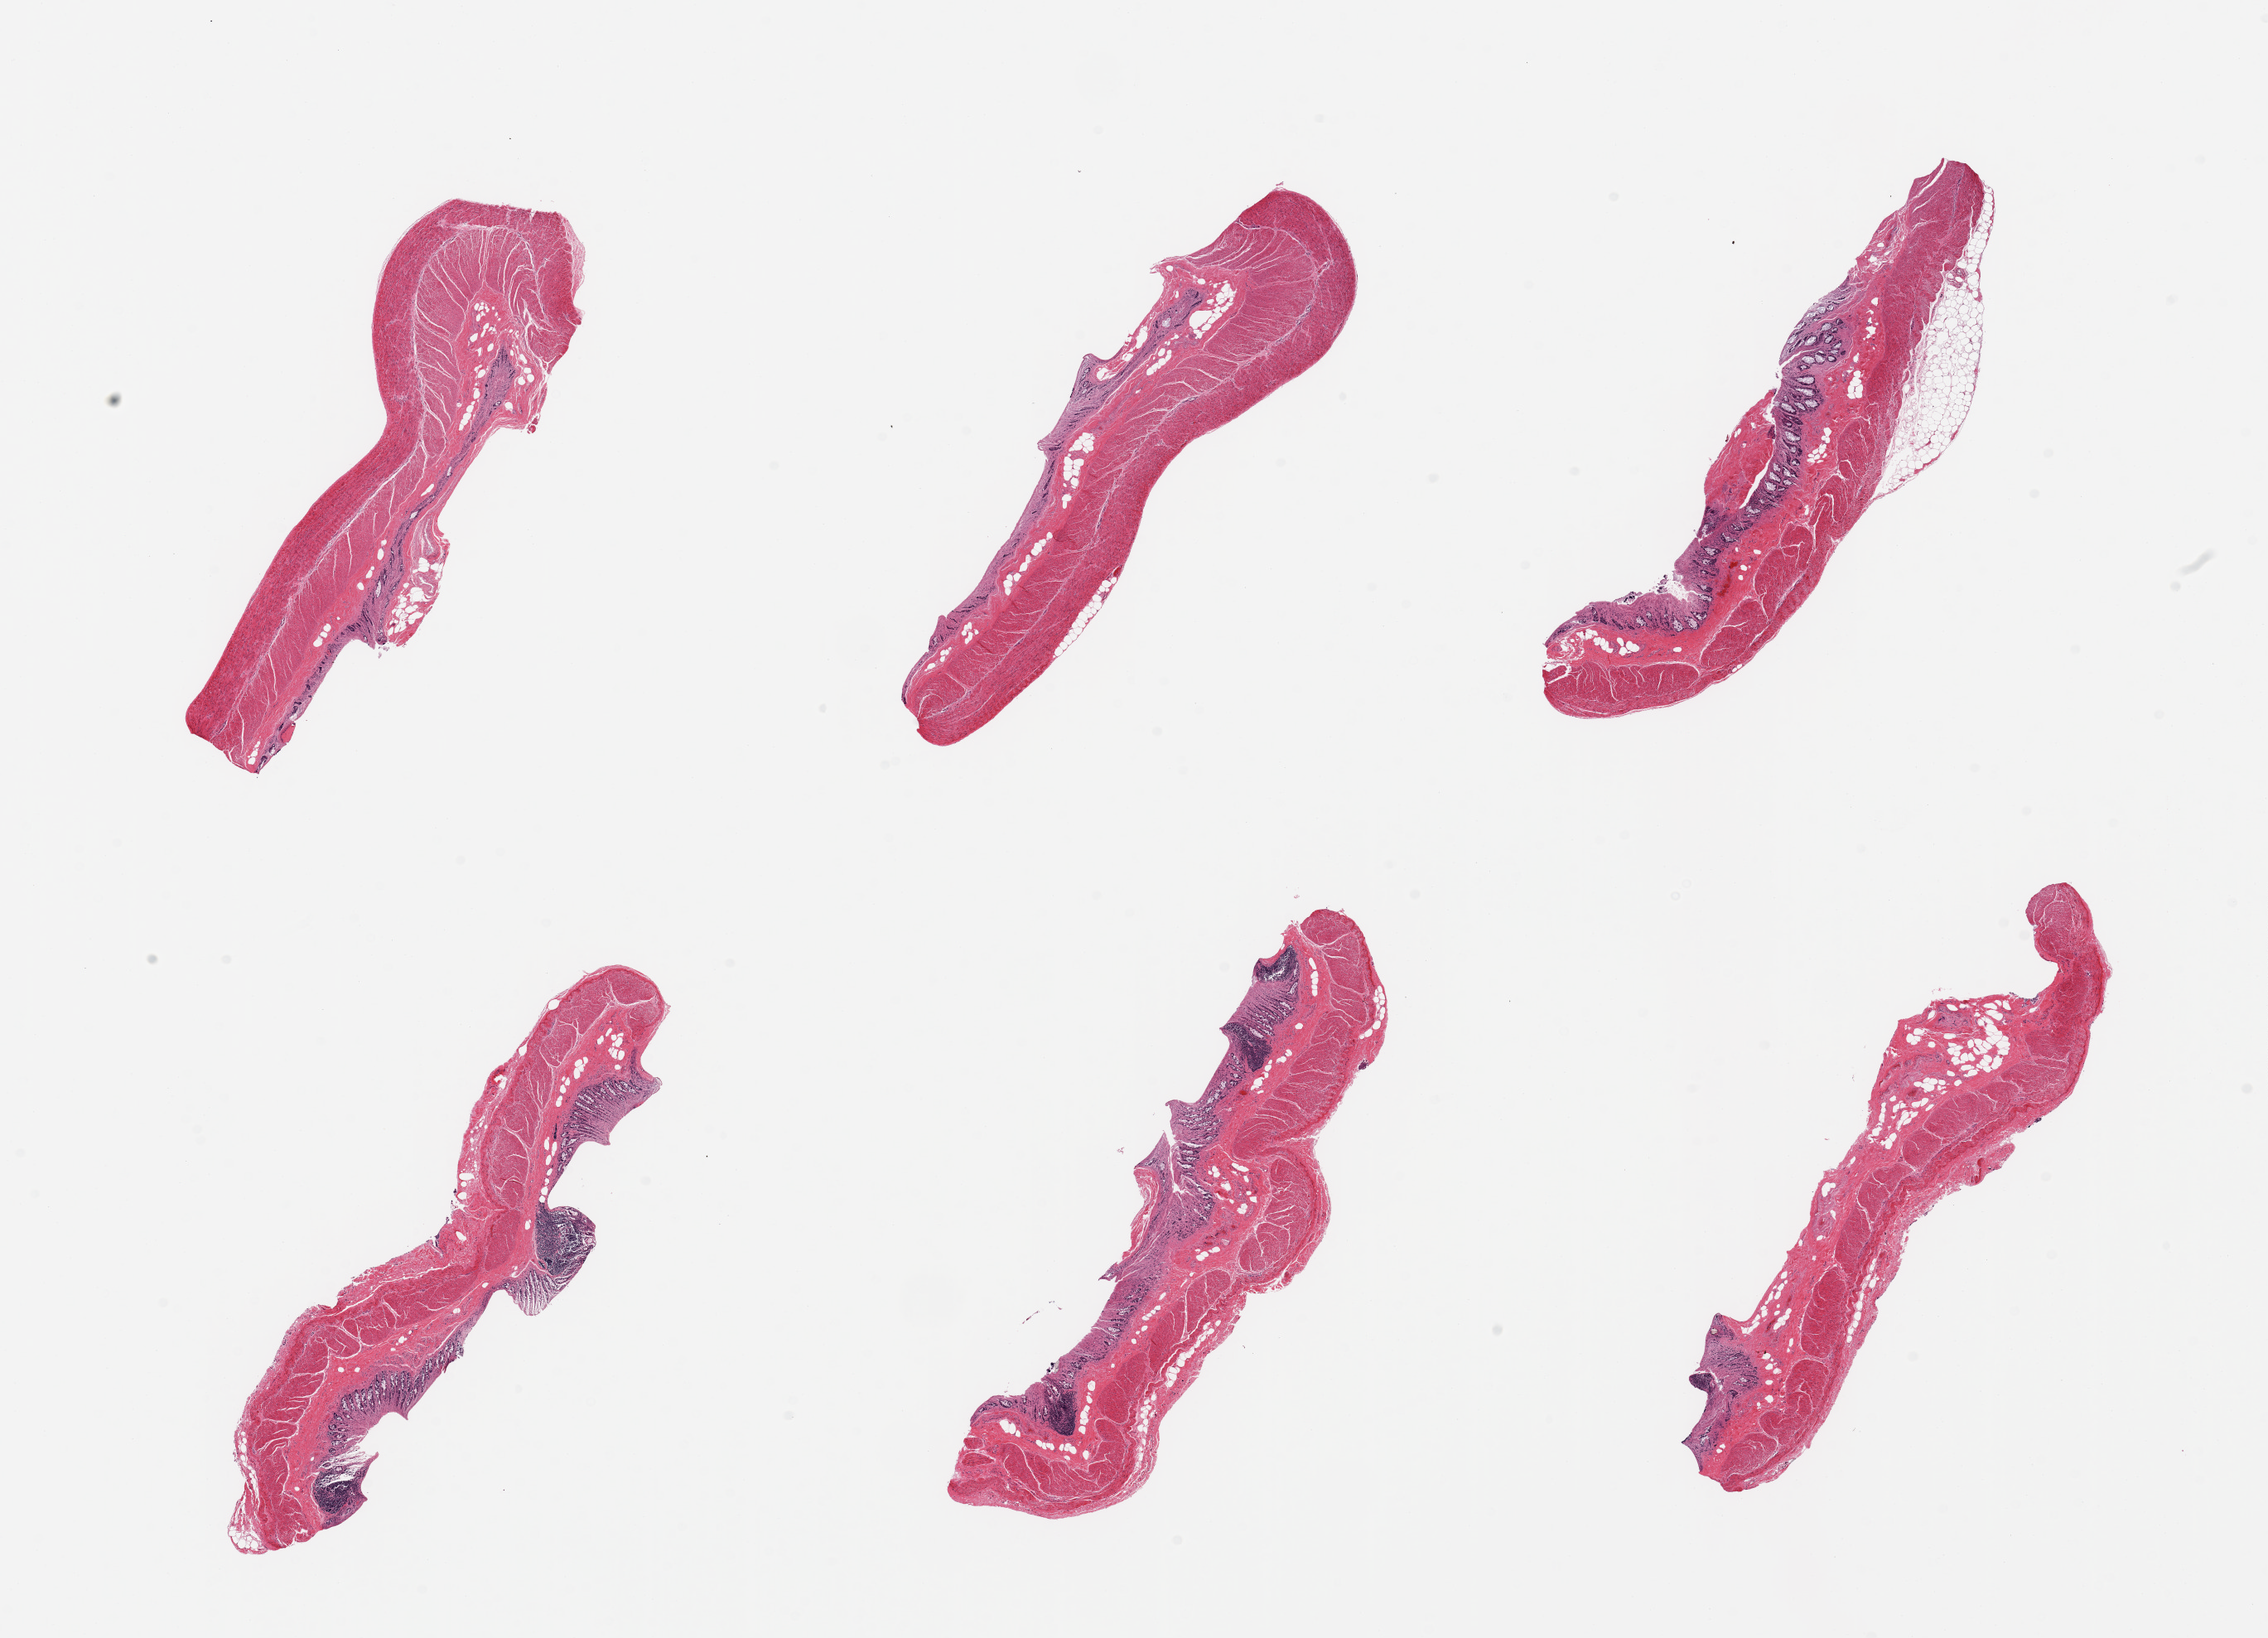
Haematoxylin and eosin whole-slide image, low-resolution overview of the scanned area, about 21.7 x 15.6 mm; PAXgene-fixed, paraffin-embedded tissue; sampled site (target tissue): transverse colon; donor tissue sample. Donor sex: female.
• reviewer comment on this tissue sample: 6 pieces, mucosa ~50% sloughed